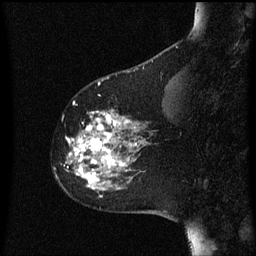
Breast MRI (dynamic contrast-enhanced), one sagittal slice. Slice 18 of 60 in the series (ordered by position). Dynamic contrast-enhanced series, image 2 of 3 at this slice position (ordered by acquisition). 1.5 T. TE 4.2 ms, TR 8 ms. 2 mm slice thickness. 256 × 256 image matrix, field of view 200 × 200 mm. Female patient, age 60 years.
Annotated regions visible in this slice (semi-automatic segmentation, software-assisted and operator-edited):
- analysis volume of interest (the breast-tissue region the enhancement analysis was run in; not a lesion): box from (x=61, y=102) to (x=150, y=197) px
- tumour enhancement mask (voxels above the 70 % enhancement threshold inside the analysis volume of interest): (x=67, y=112)–(x=138, y=185)